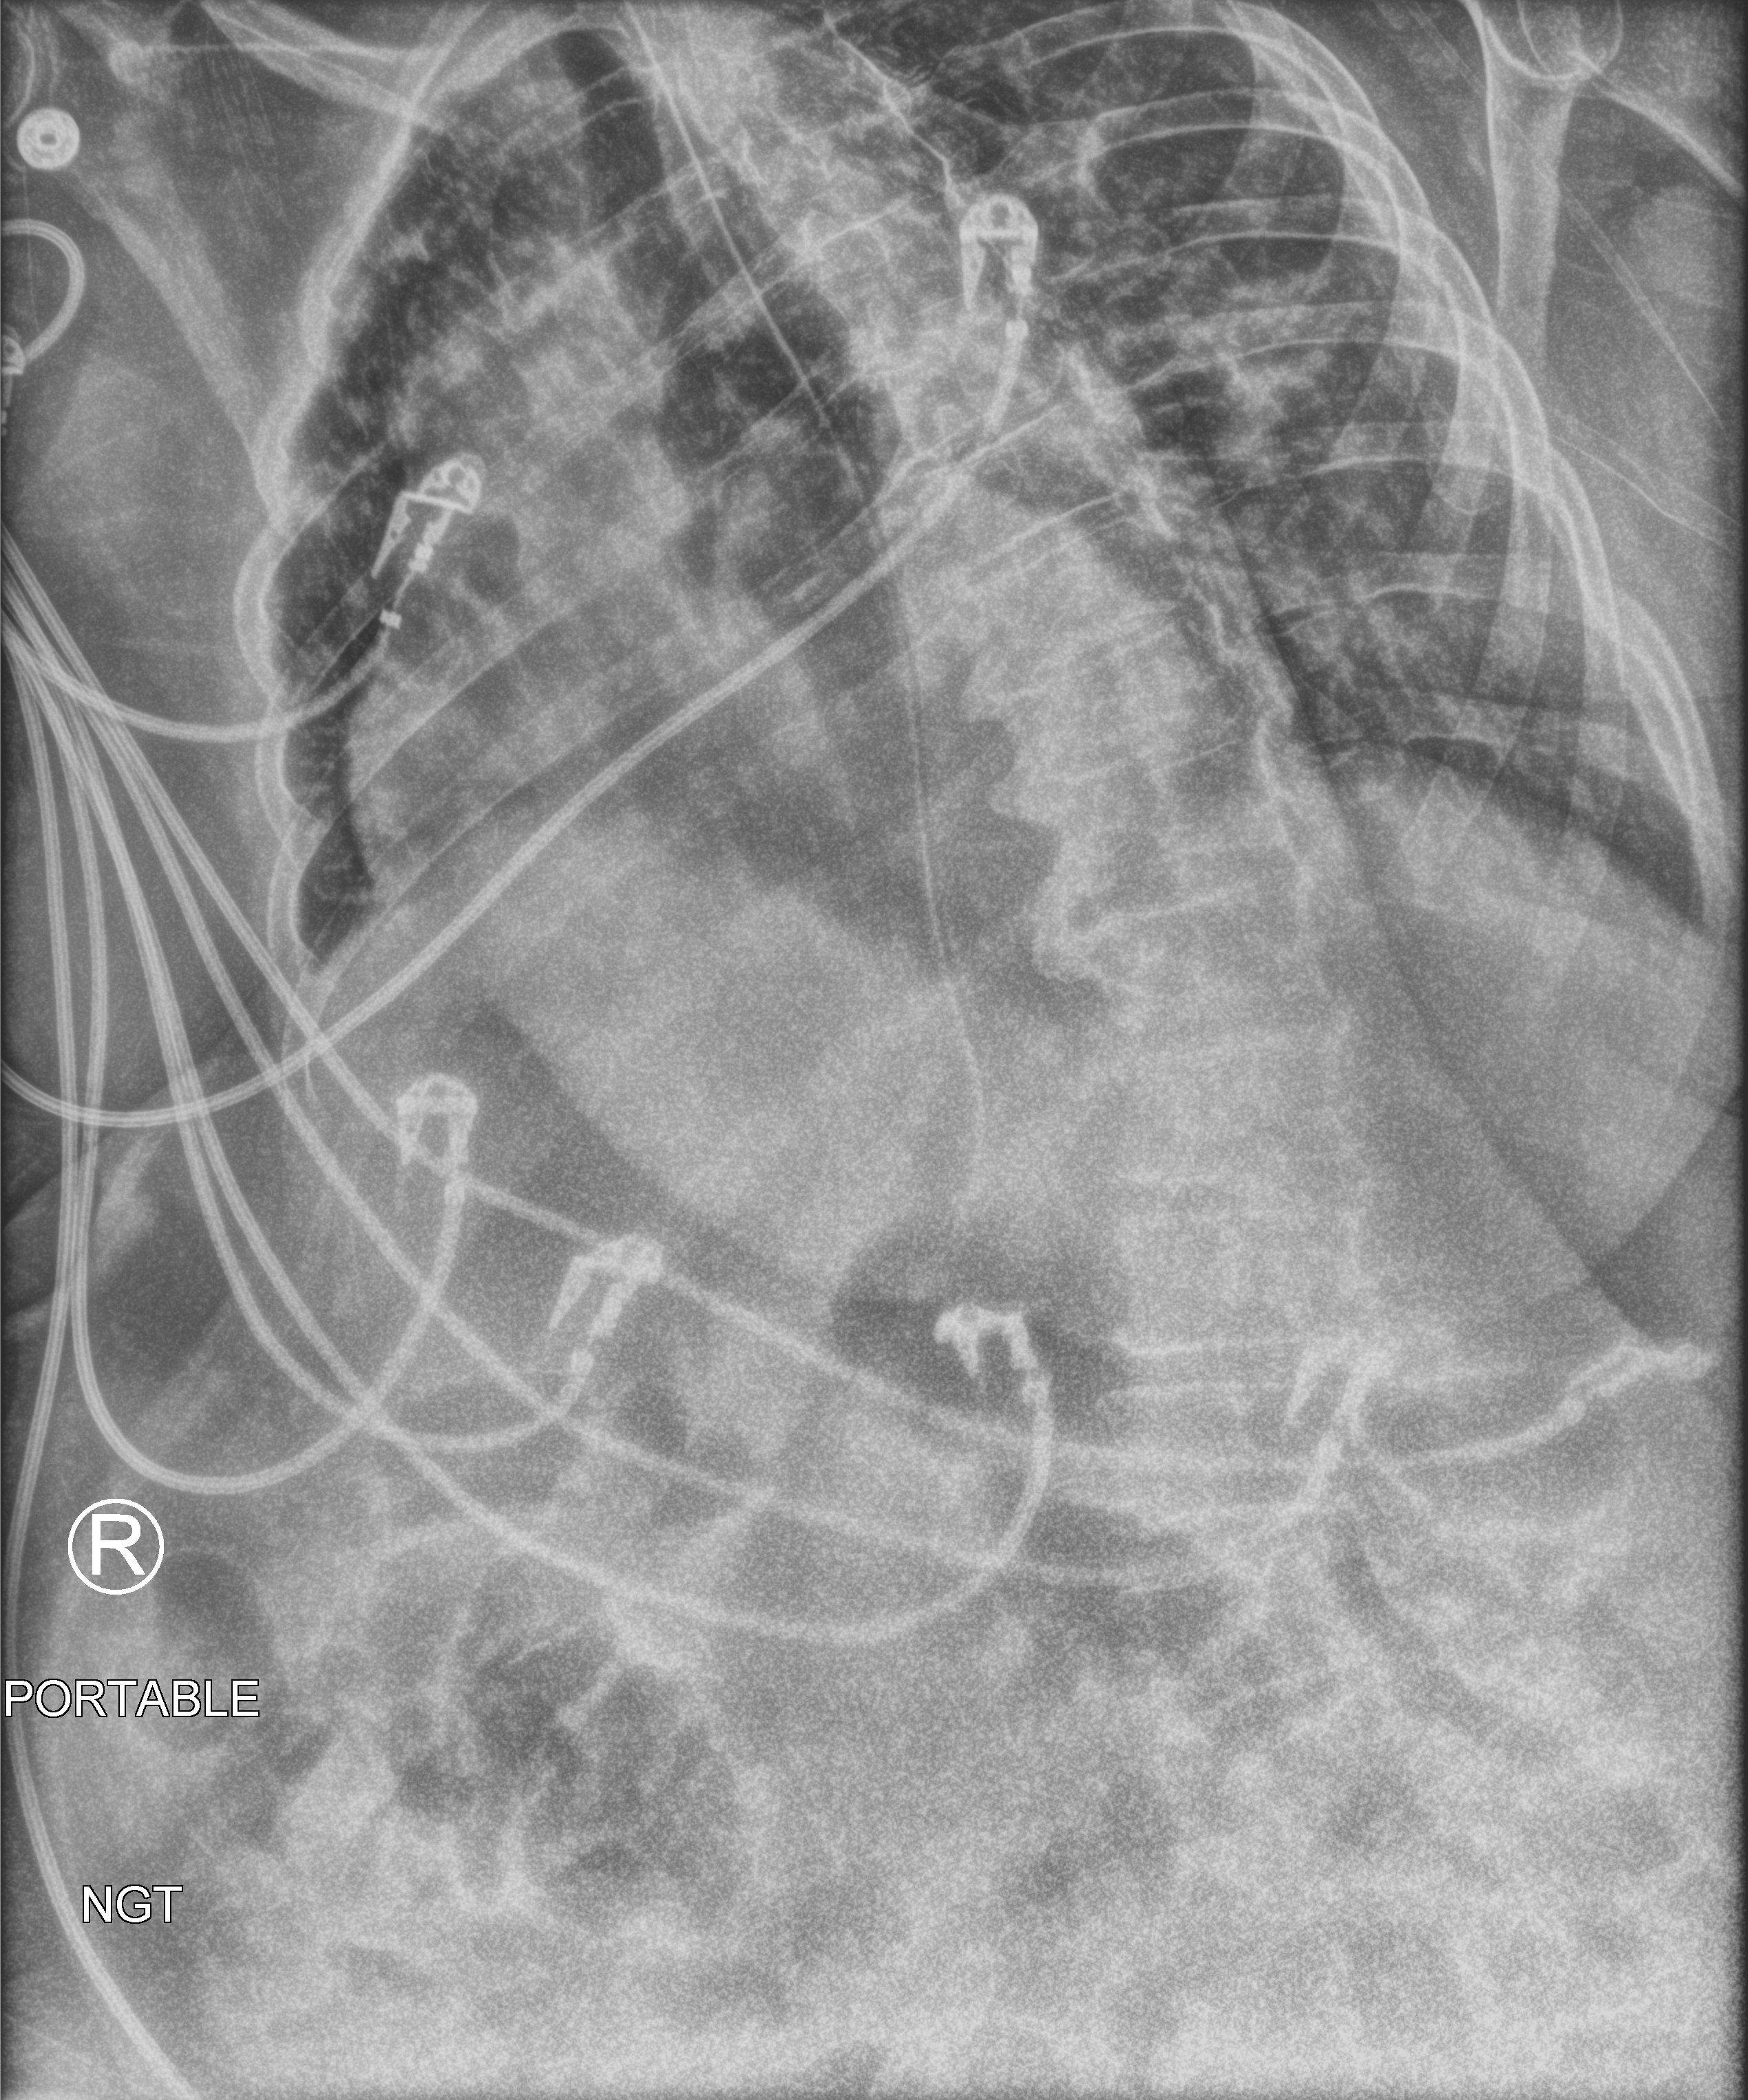
Abdomen radiograph; anteroposterior (AP) projection. Female patient hospitalised with COVID-19, age 75–90 years.
Hospital-stay facts (about this admission, not read from this image; timing relative to this image not recorded):
- chronic kidney disease (admission record): no
- mechanically ventilated during this hospital stay: yes
- COPD (admission record): yes